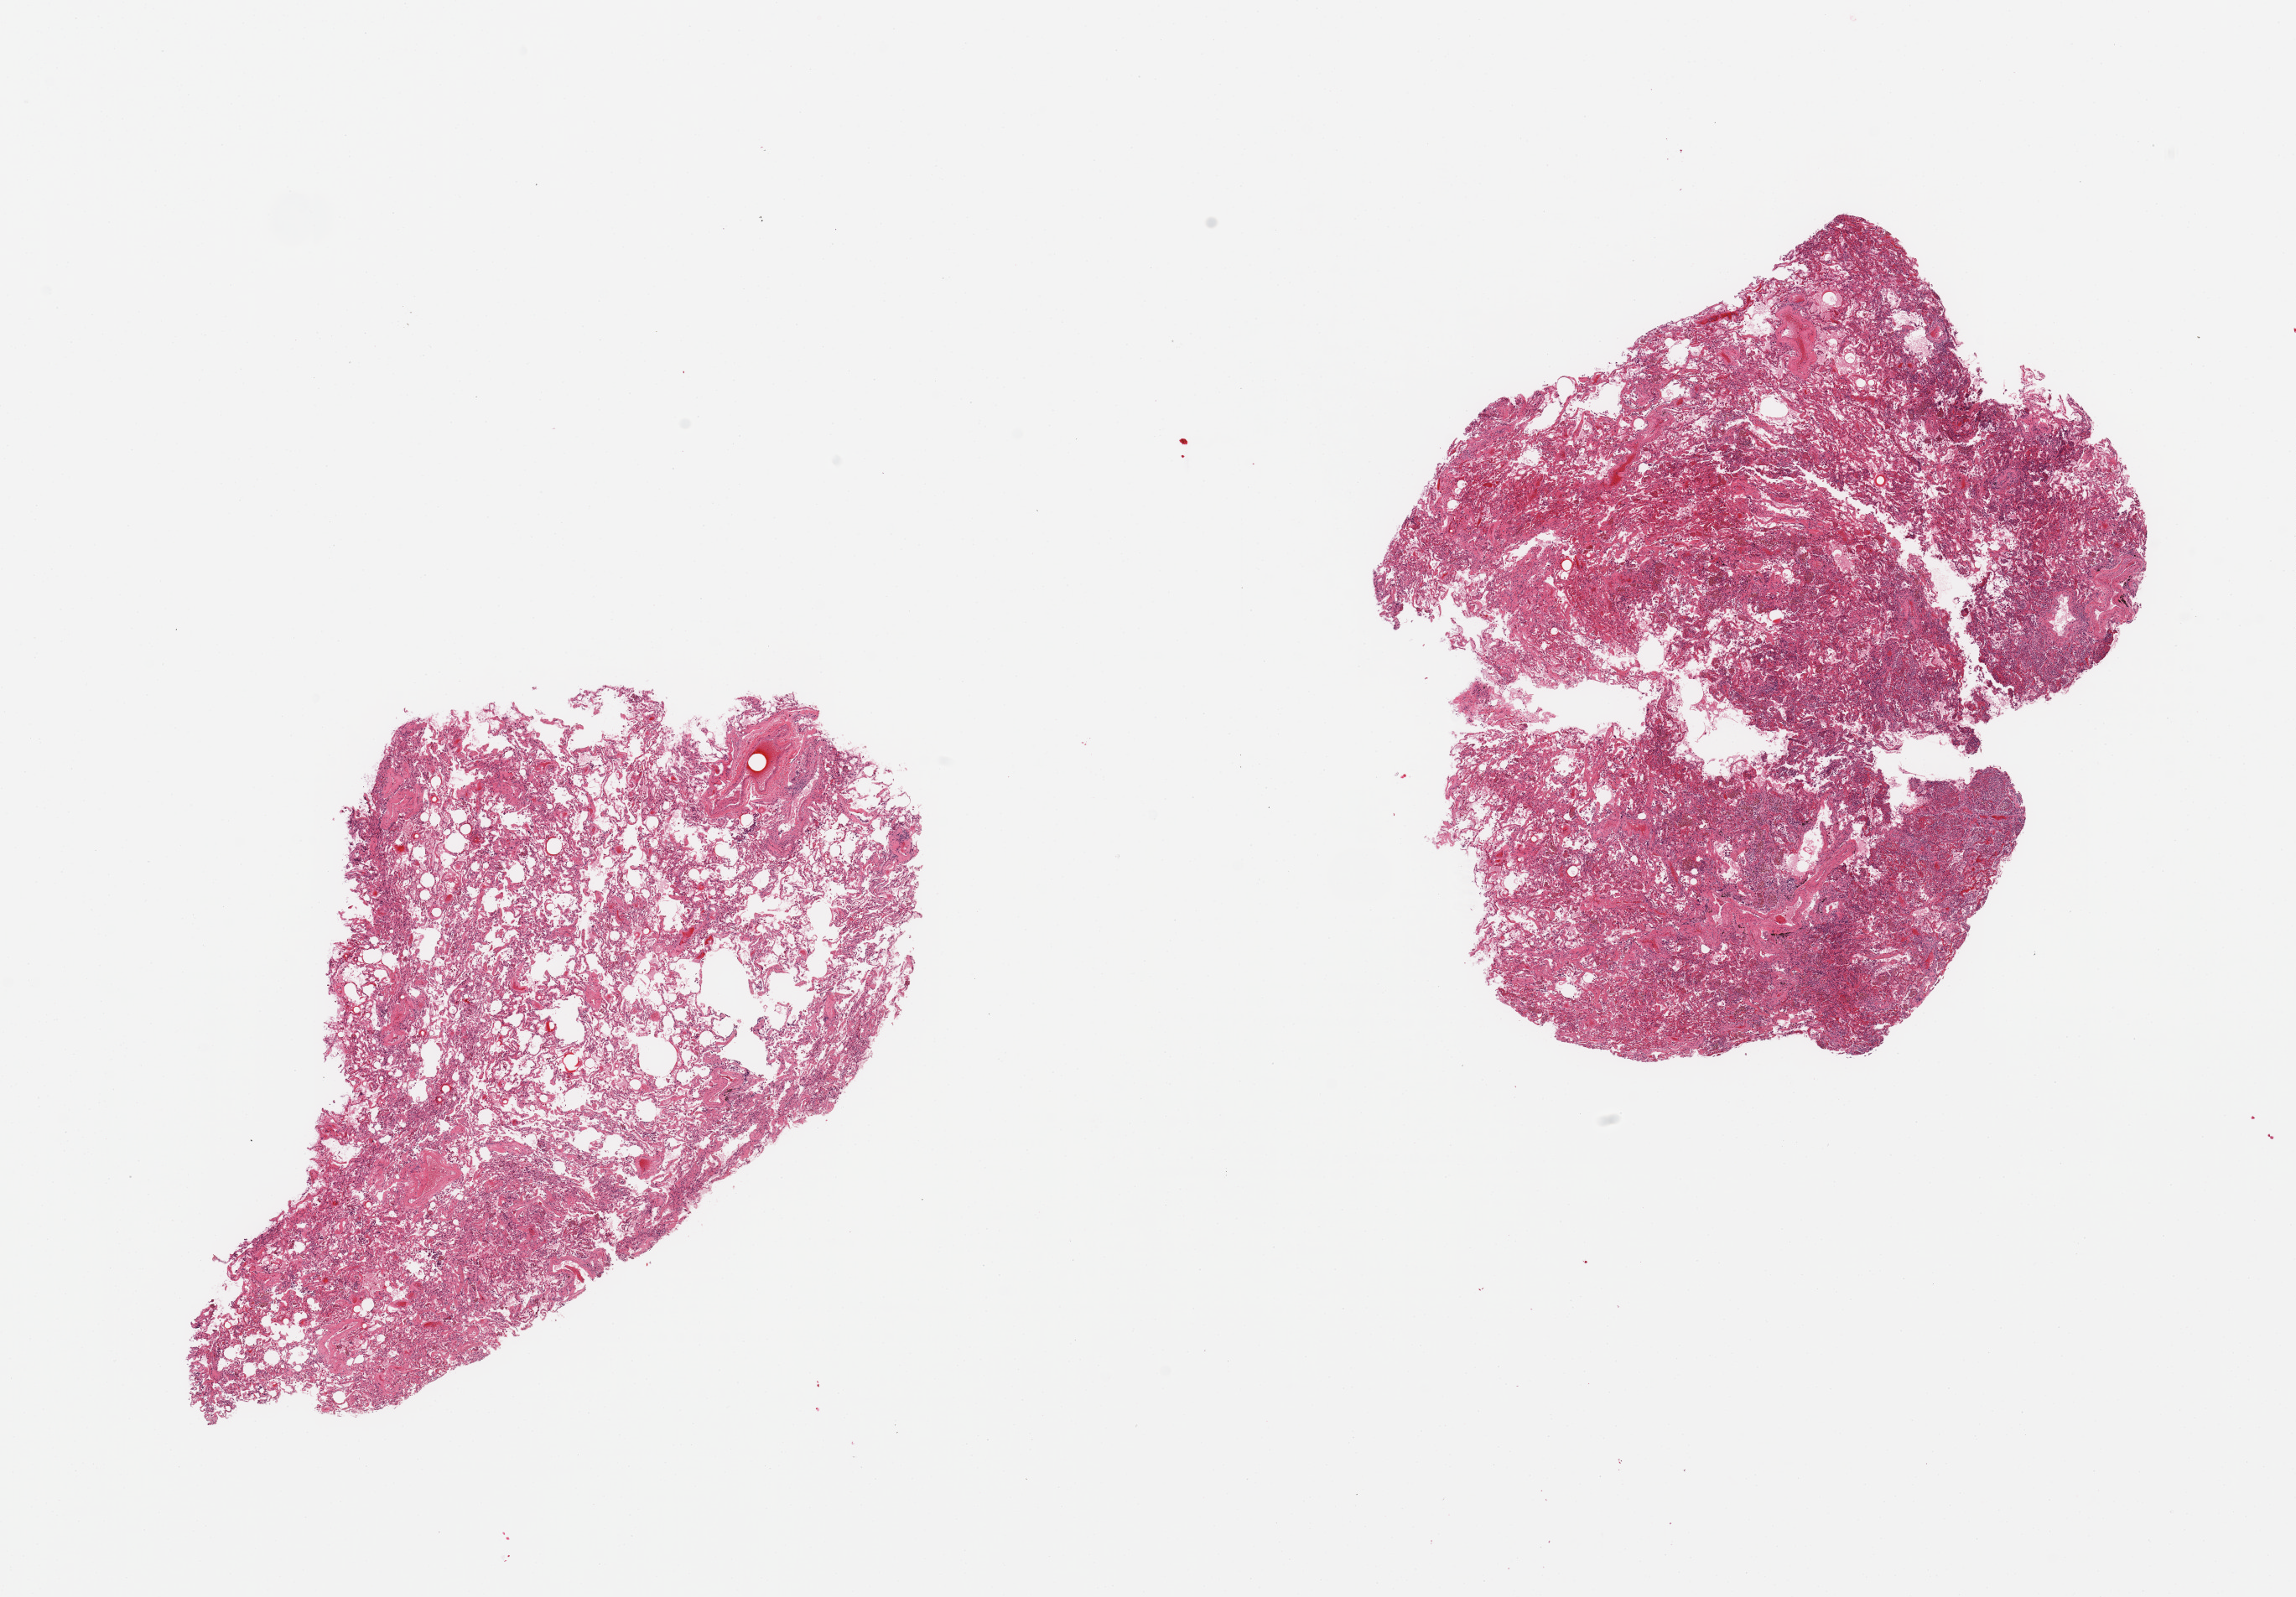
Whole-slide image, H&E stain — whole scanned area (about 21.7 x 15.1 mm, slide scanned at 20x) shown as a low-resolution overview, PAXgene-fixed paraffin-embedded (PFPE) section, sampled site (target tissue): lung, donor tissue sample. Donor: male.
Review note (as recorded): 2 pieces; patchy pneumonia; numerous intraalveolar pigmented macrophages; mild to moderate interstitial fibrosis.